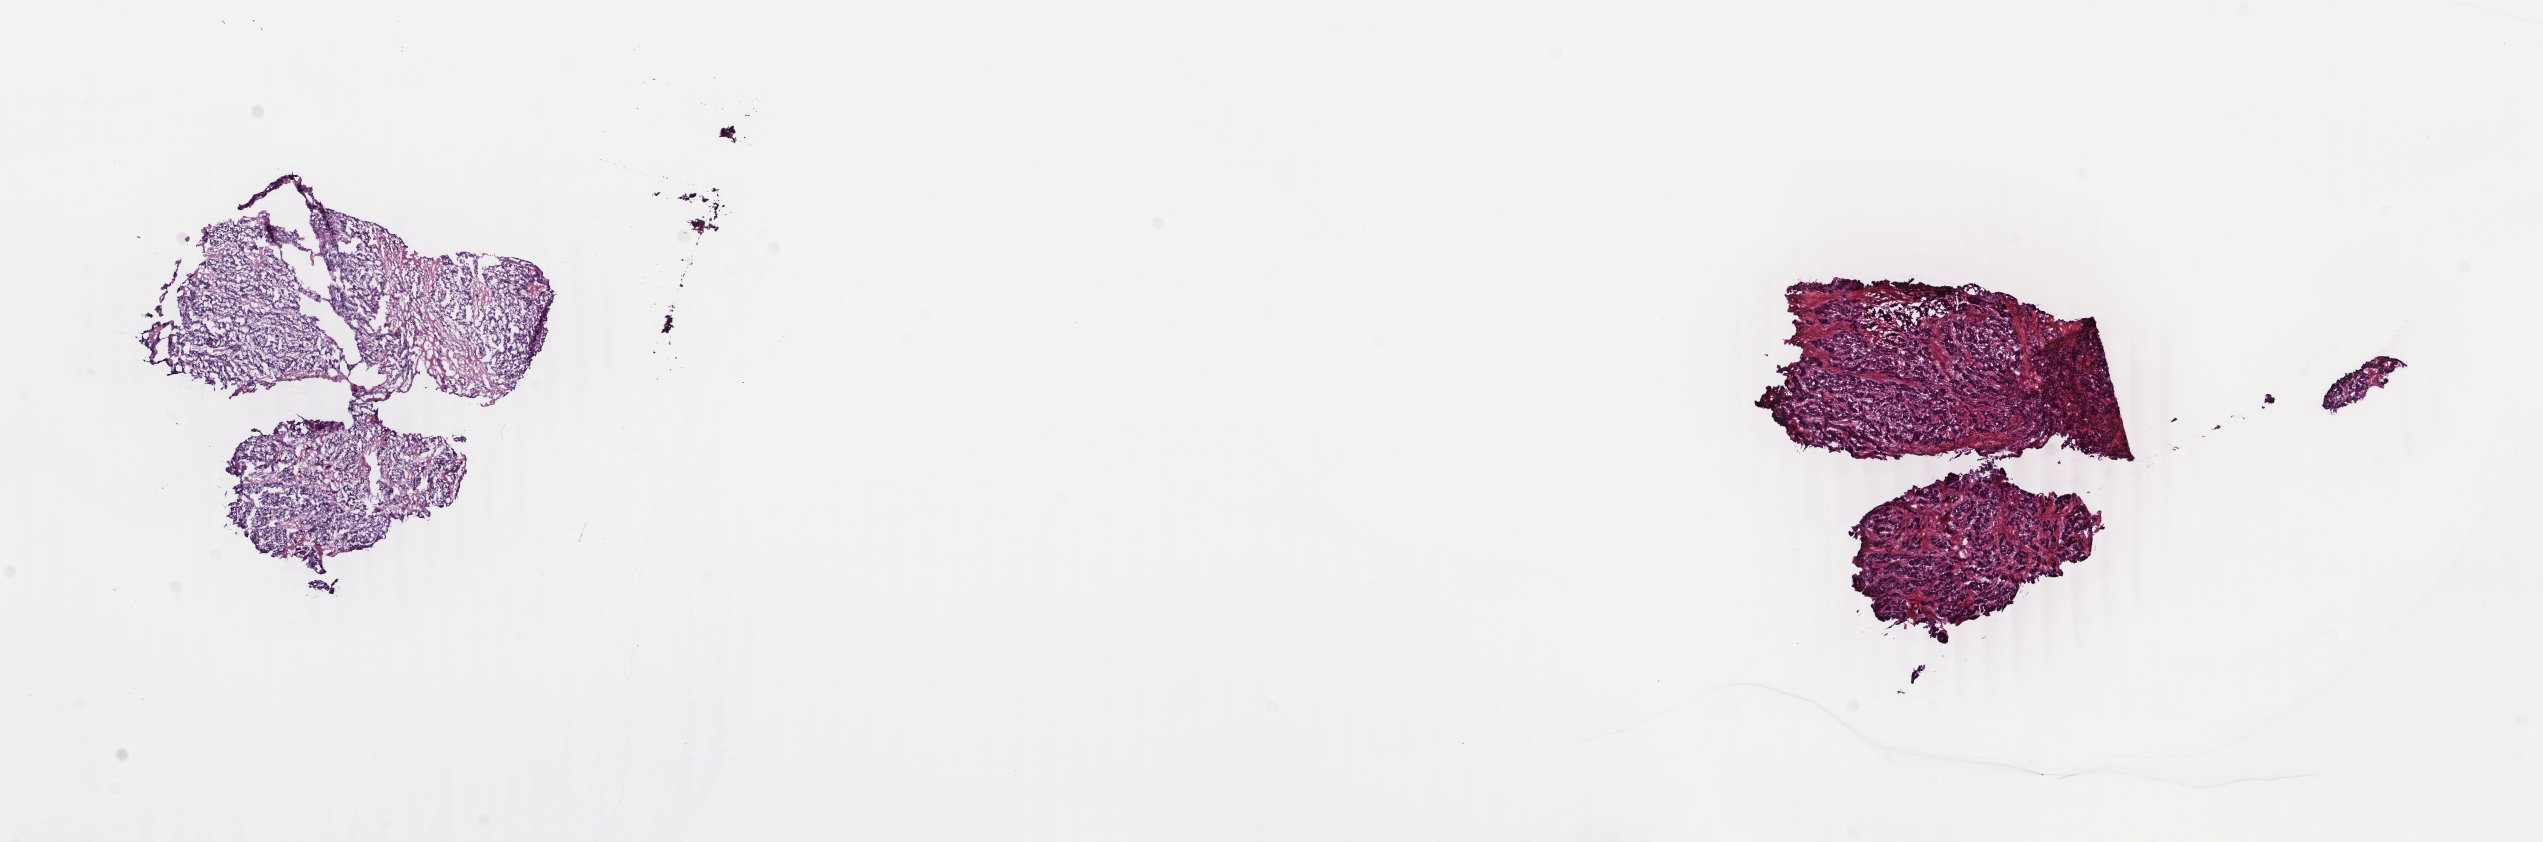
Whole-slide histology image, H&E — shown as a low-resolution overview of the whole scanned area (about 20.2 x 6.7 mm), frozen section from the top of the tissue portion, sample: primary tumour, liver. Patient: female, age at initial diagnosis 68 years. Histologic grade: G3 (poorly differentiated). Pathologist review of this section (percent, as recorded): tumour cells 50%, tumour nuclei 60%, normal cells 0%, stromal cells 50%, necrosis 0%. Inflammatory infiltration, as recorded: lymphocyte infiltration 0%, monocyte infiltration 0%, neutrophil infiltration 0%.
AJCC pathologic stage: II. Histologic diagnosis: Hepatocellular carcinoma, NOS.